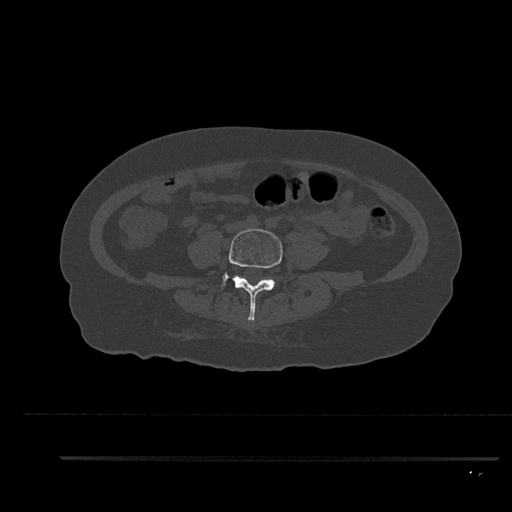
CT including the spine, one axial slice; position 13 of 797 along the scan axis; 120 kVp; bone window (W 1800 / L 400 HU); 0.5 mm slice thickness; 512 × 512 image matrix. Female patient, age 44 years. Case-level facts recorded for this patient, not image findings: primary cancer: renal; vertebrae with lytic lesions (as recorded): L1.
Structures marked on this image (semi-automatic segmentation, software-assisted and operator-edited):
- L4 vertebra: bounding box <221,229,283,321> (left, top, right, bottom; pixels)